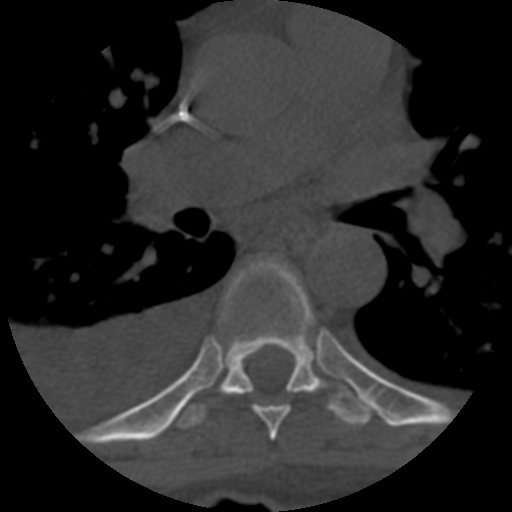
CT including the spine, one axial slice; position 425 of 708 along the scan axis; 120 kVp; one of 3 acquisitions stored at this slice position; bone window (W 1800 / L 400 HU); 512 × 512 image matrix, field of view 160 × 160 mm. Patient age 55 years. From the clinical record (not read from this slice): primary cancer: colon; vertebrae with lytic lesions (as recorded): T12, L1, L5.
Structures marked on this image (semi-automatically segmented with operator editing):
- T6 vertebra: bounding box <253,405,290,441> (left, top, right, bottom; pixels)
- T7 vertebra: <177,257,373,430>